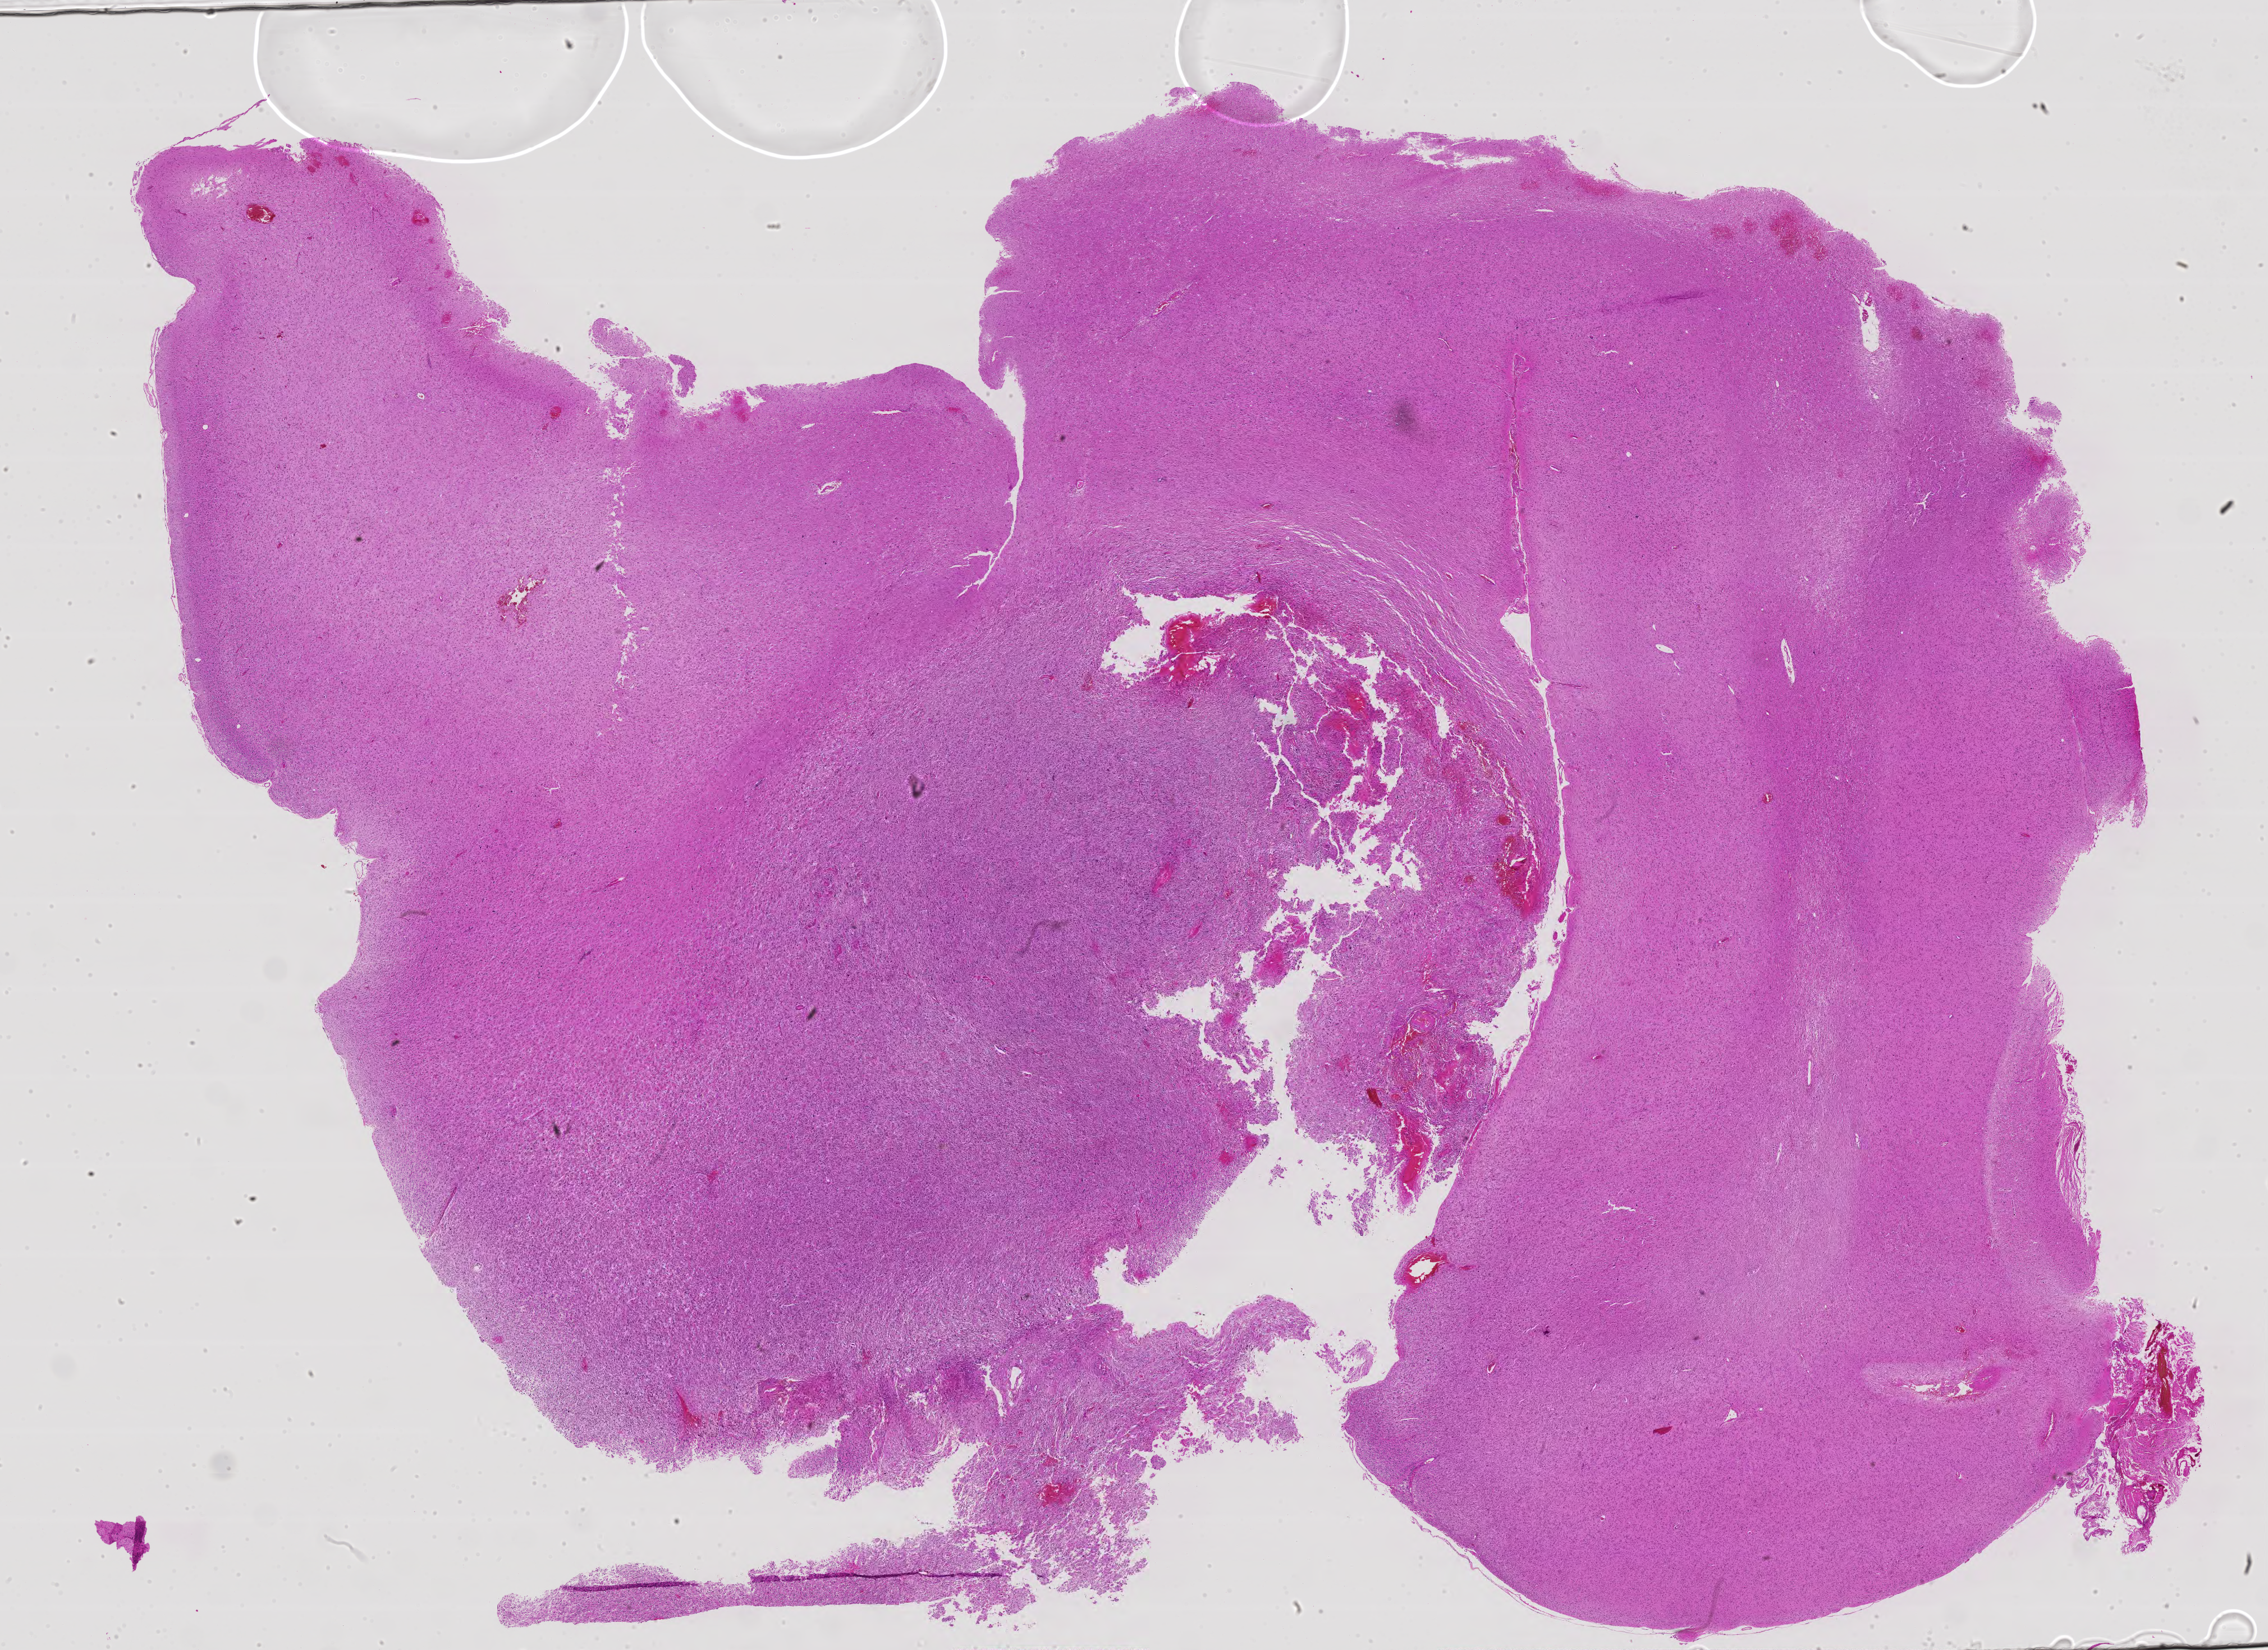
Digitized Hematoxylin and eosin (H&E) stained tissue section (whole slide) — low-resolution overview of the scanned area, about 32.3 x 23.5 mm; FFPE section; primary tumour sample from the brain. Male patient; age at initial diagnosis 57 years. Histologic grade: G3 (poorly differentiated).
• laterality: left
• pathologic diagnosis: Astrocytoma, anaplastic